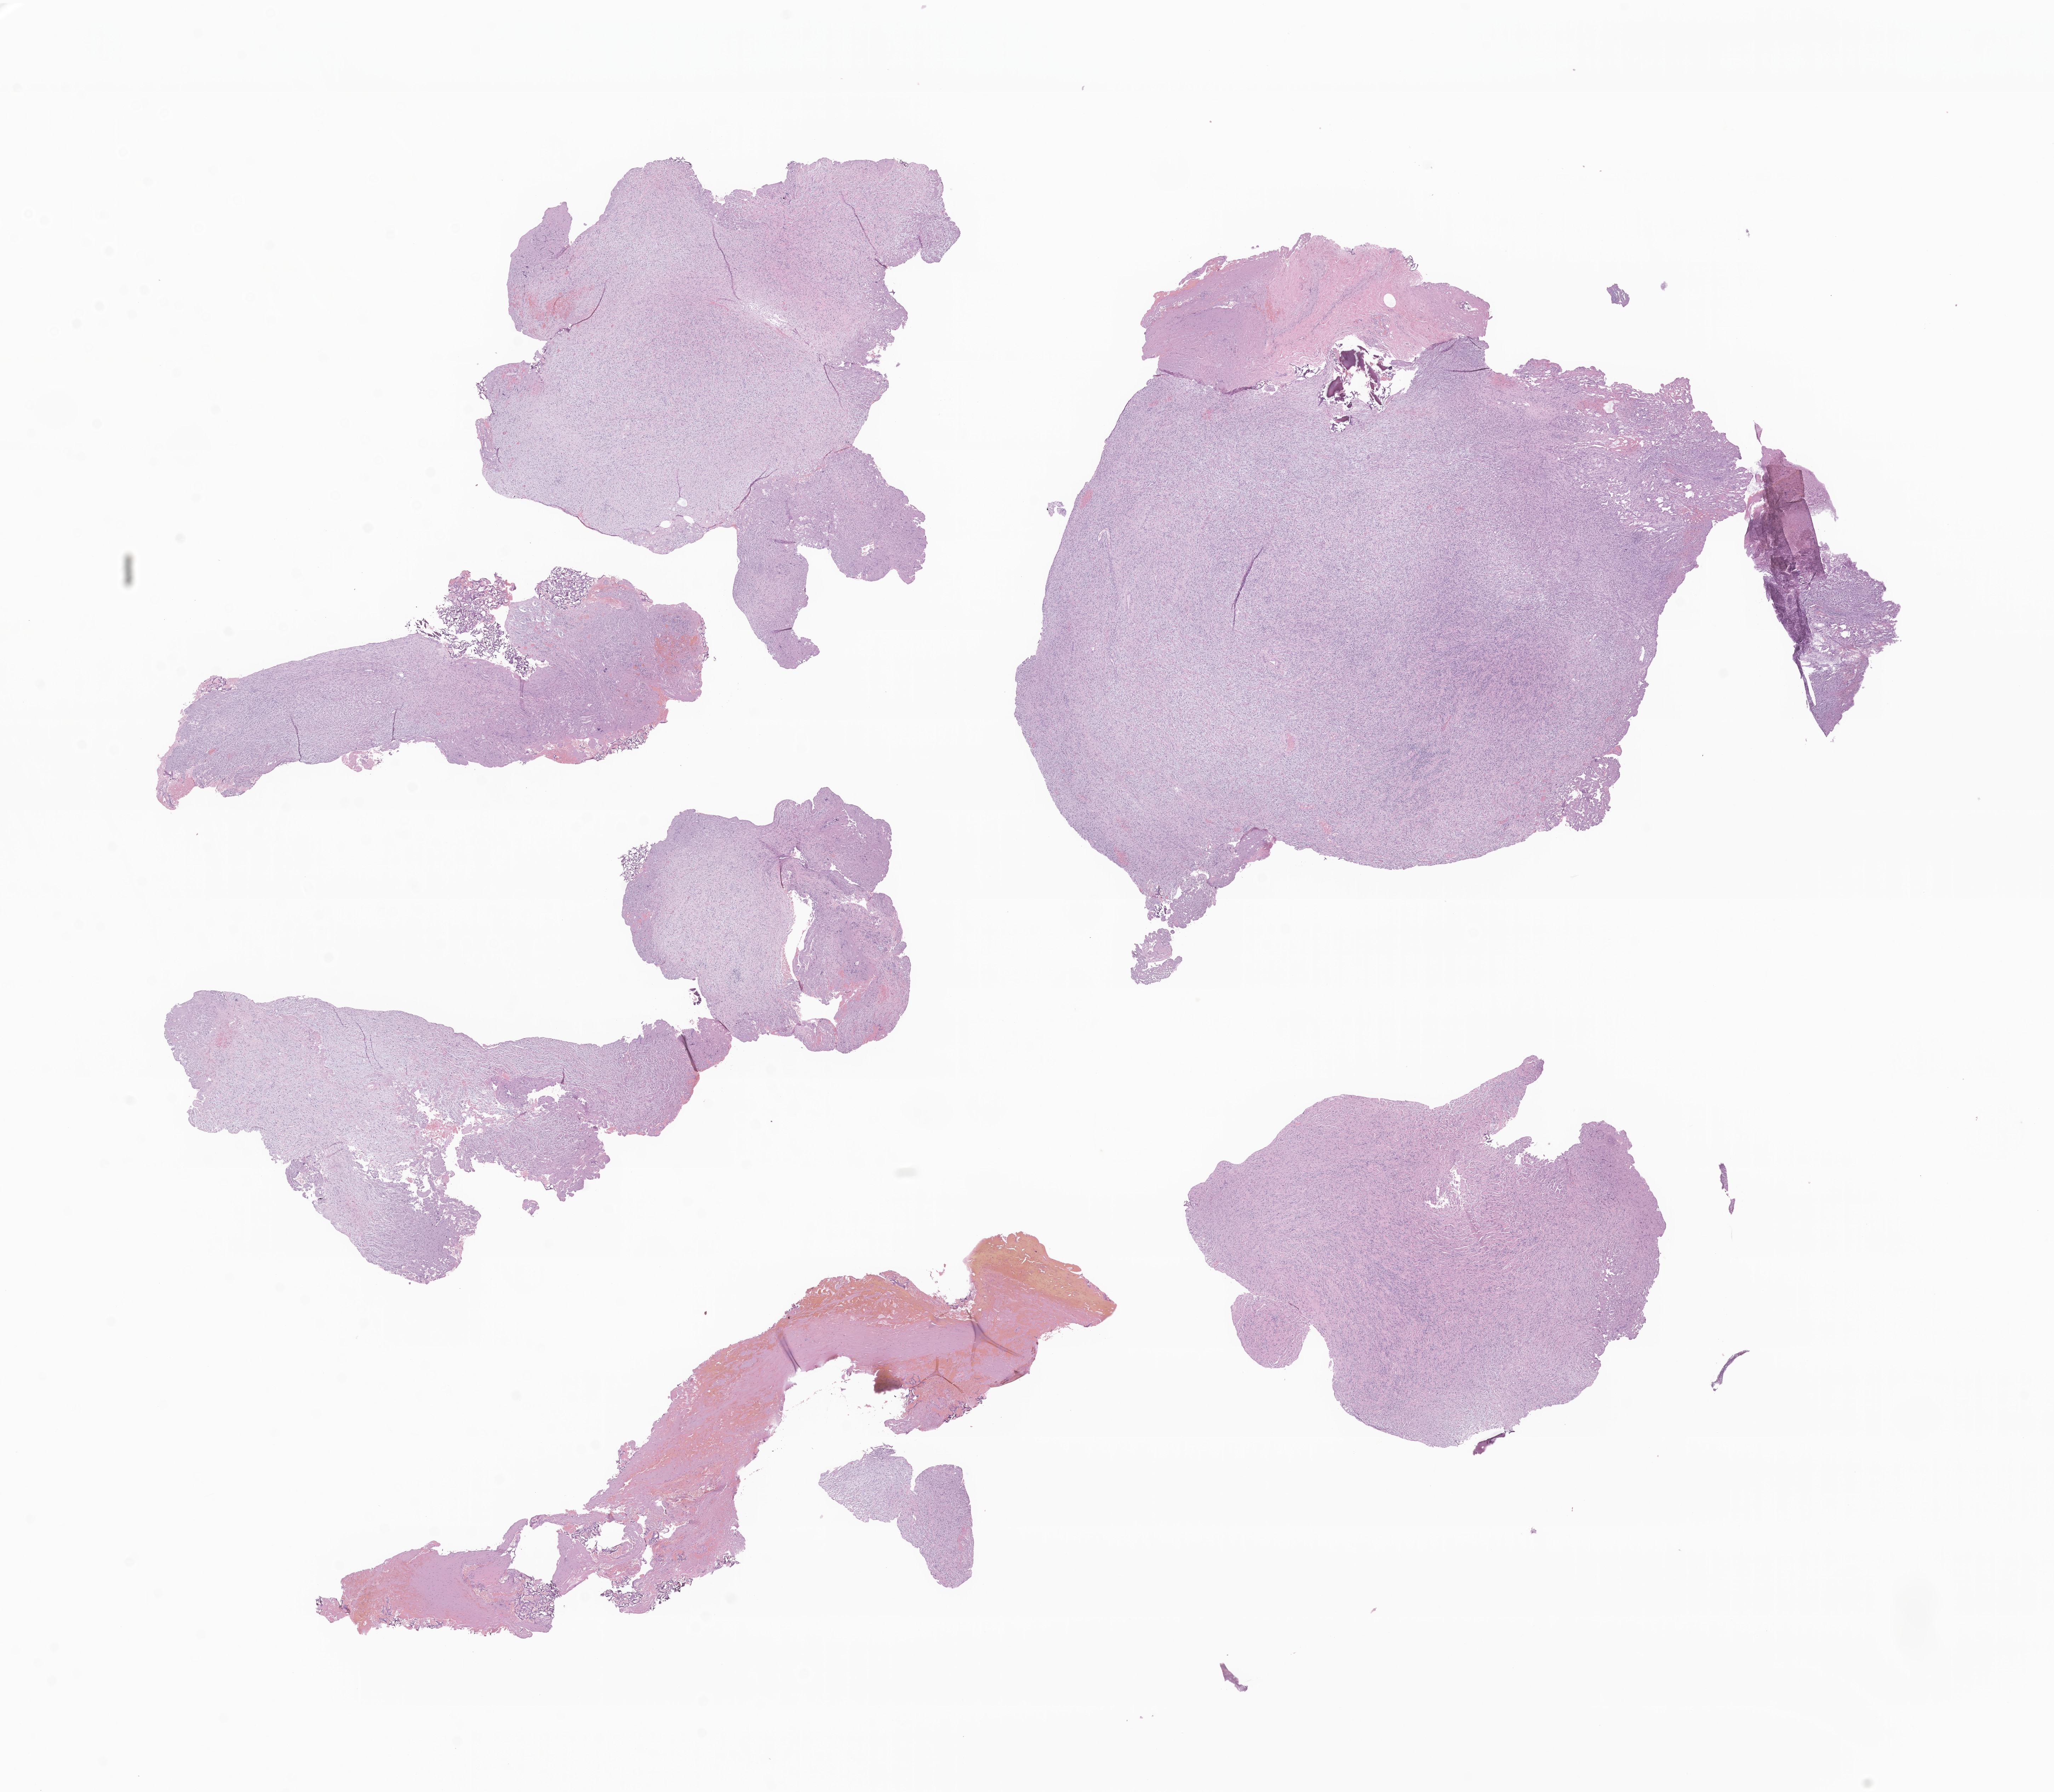
Hematoxylin and eosin (H&E) whole-slide image of tumor tissue from the spinal cord, a low-resolution overview of the entire scanned area, about 24.5 x 21.3 mm; formalin-fixed, paraffin-embedded (FFPE) tissue. Male patient, age 191 months (15 years 11 months).
Recorded diagnosis: Neurofibroma, NOS.